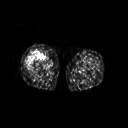
FDG PET of an extremity soft-tissue mass (from a PET/CT study), one axial slice; slice 223 of 311 in the series (ordered by position); 128 × 128 image matrix. Female patient, age 57 years. Case-level facts recorded for this patient, not image findings: histological type: pleiomorphic undifferentiated sarcoma; grade: high; site of the primary tumour: right quadricep.
Structures marked on this image (expert contour drawn on MRI and transferred to this co-registered scan by the dataset authors):
- tumour plus oedema (research contour): bounding box <26,50,41,69> (left, top, right, bottom; pixels)